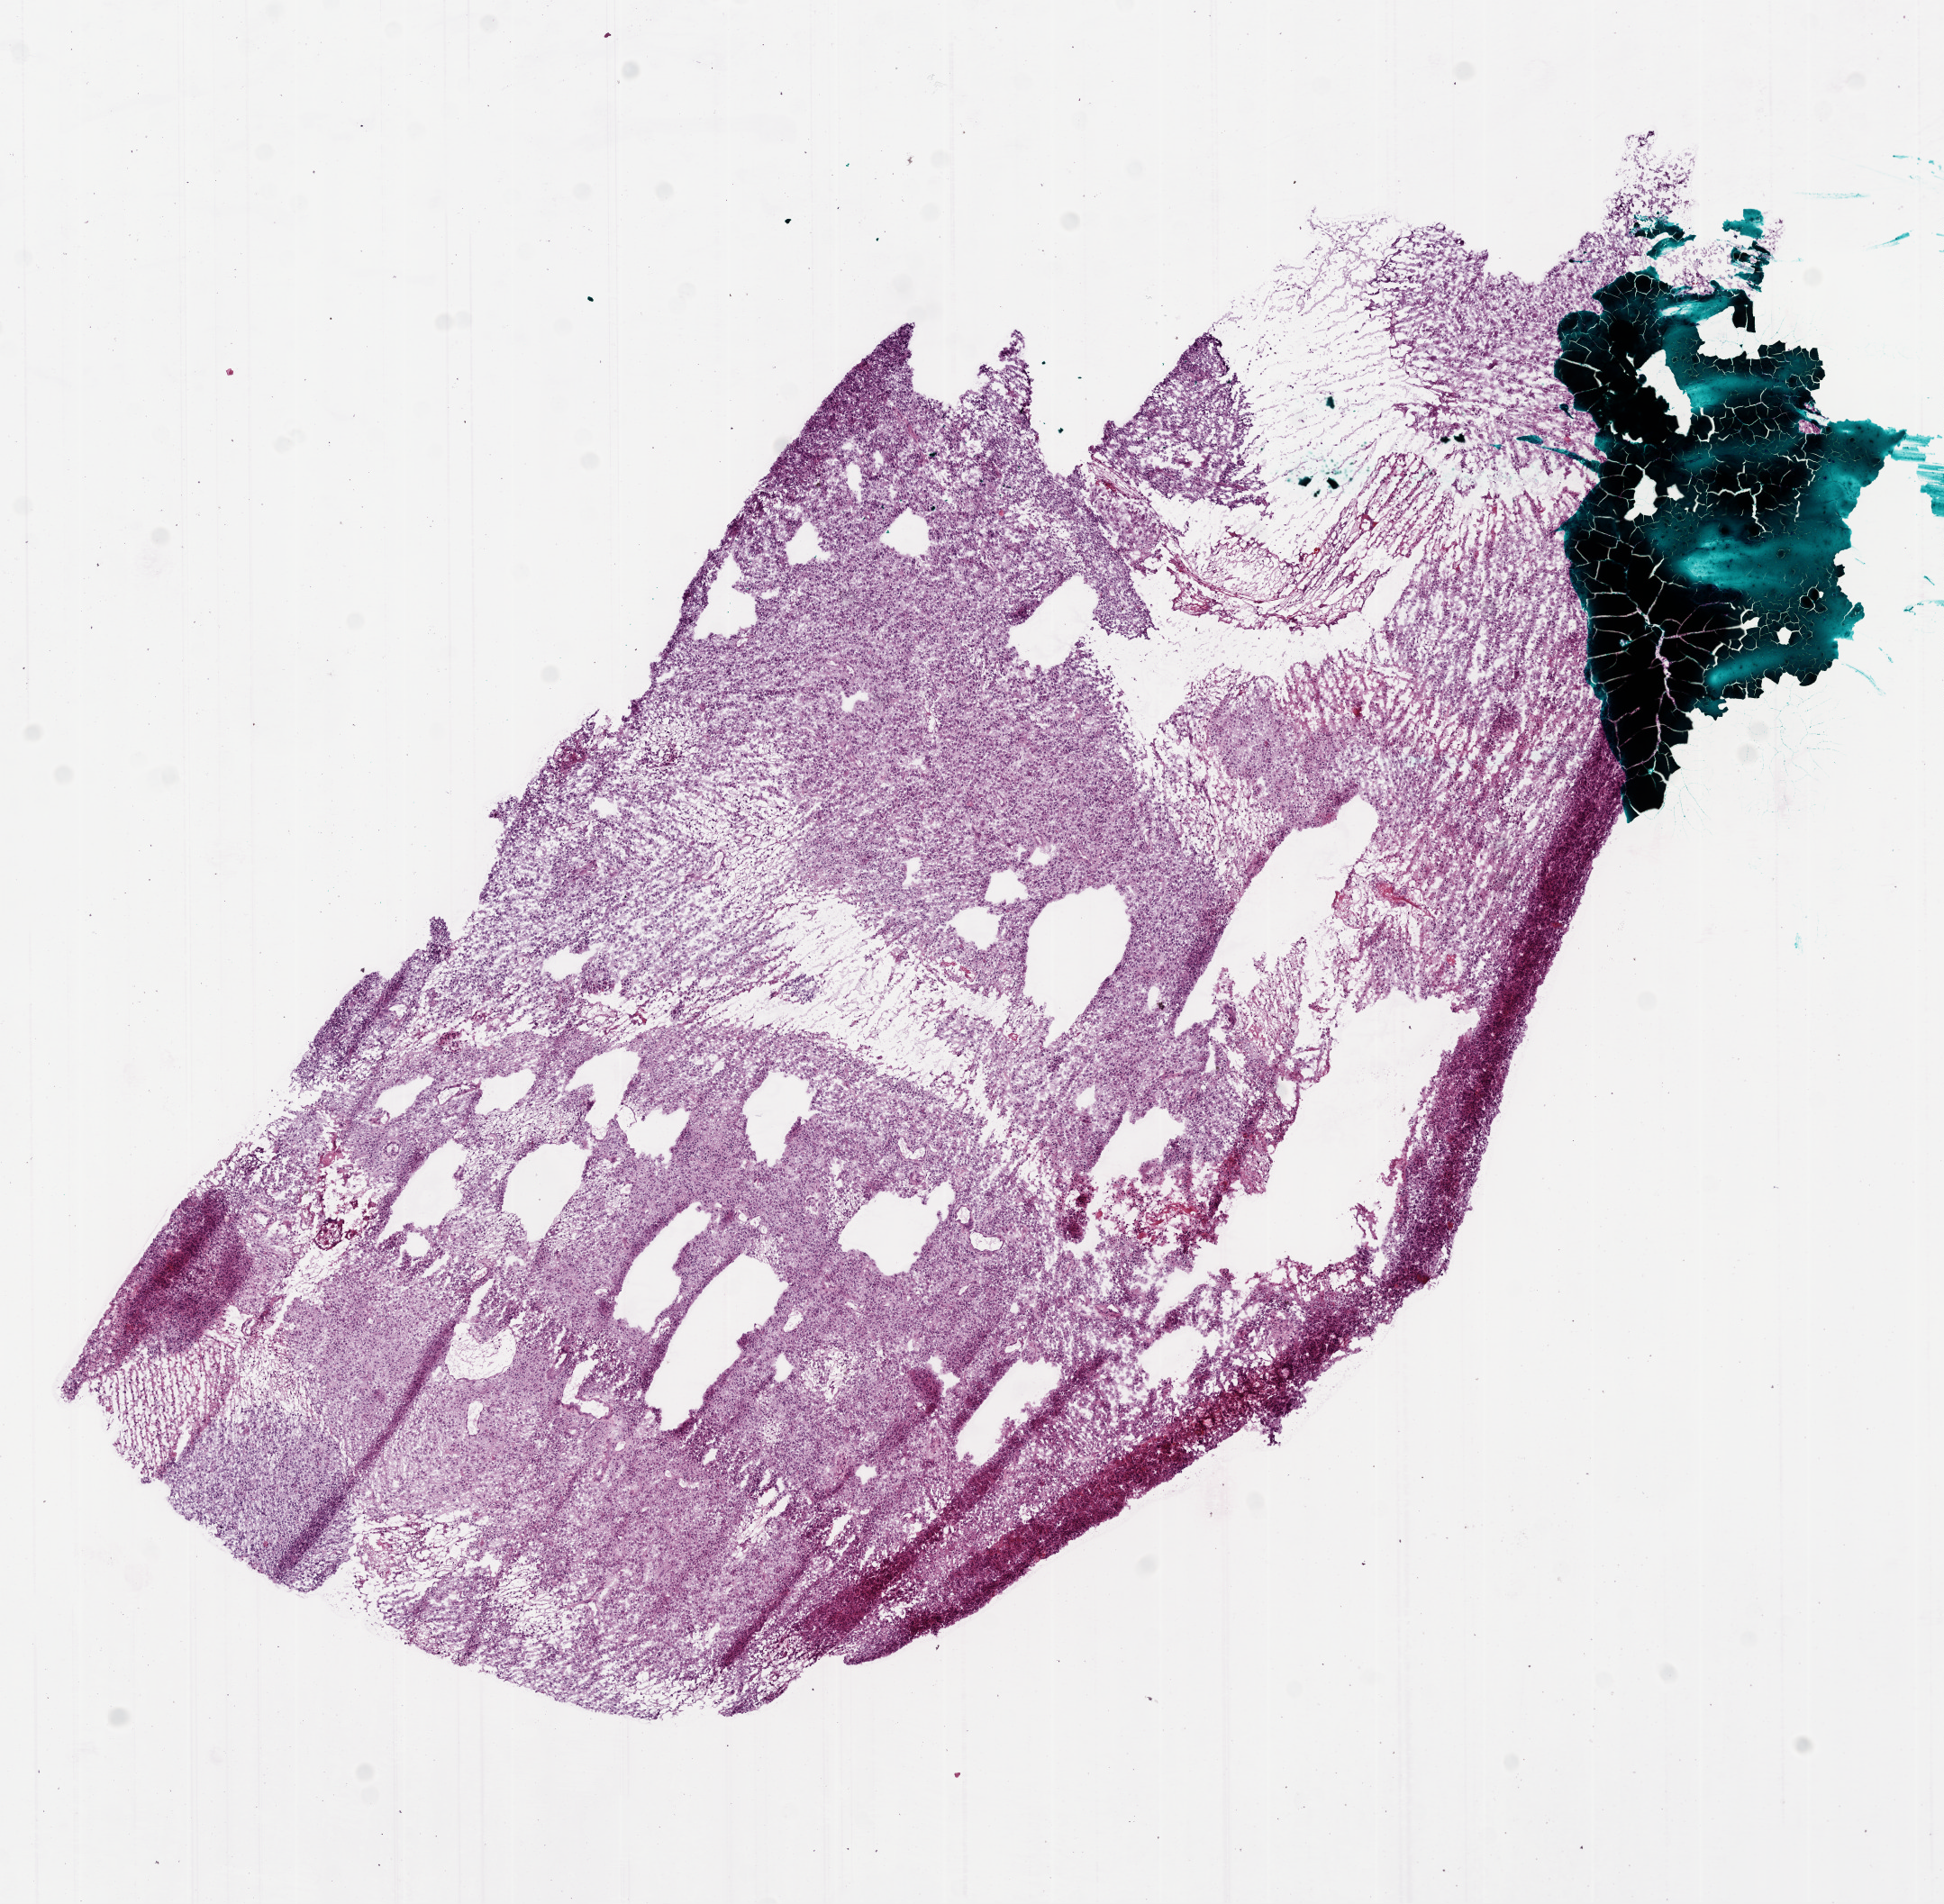
H&E whole-slide image — shown as a low-resolution overview of the whole scanned area (about 8.7 x 8.5 mm), frozen section from the bottom of the tissue portion, brain, primary tumour sample. Male, age 52 years at initial diagnosis. Composition of this section per pathologist review: tumour cells 85%, tumour nuclei 90%, normal cells 0%, stromal cells 5%, necrosis 10%.
Histologic diagnosis: Glioblastoma.